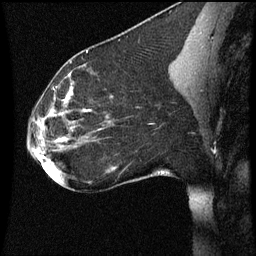
Breast MRI (dynamic contrast-enhanced), one sagittal slice; position 29 of 60 along the scan axis; dynamic contrast-enhanced series, image 2 of 3 at this slice position (ordered by acquisition); 1.5 T; TE 4.2 ms, TR 8.9 ms; 256 × 256 image matrix. Female patient, age 35 years. From the clinical record (not read from this slice): setting: breast cancer imaged before/during neoadjuvant chemotherapy; receptor status: HER2-positive.
Outlined on this slice (semi-automatic segmentation, software-assisted and operator-edited):
- analysis volume of interest (the breast-tissue region the enhancement analysis was run in; not a lesion): bounding box (x1, y1, x2, y2) in pixels: (26, 66, 177, 177)
- tumour enhancement mask (voxels above the 70 % enhancement threshold inside the analysis volume of interest): (65, 92, 73, 103)